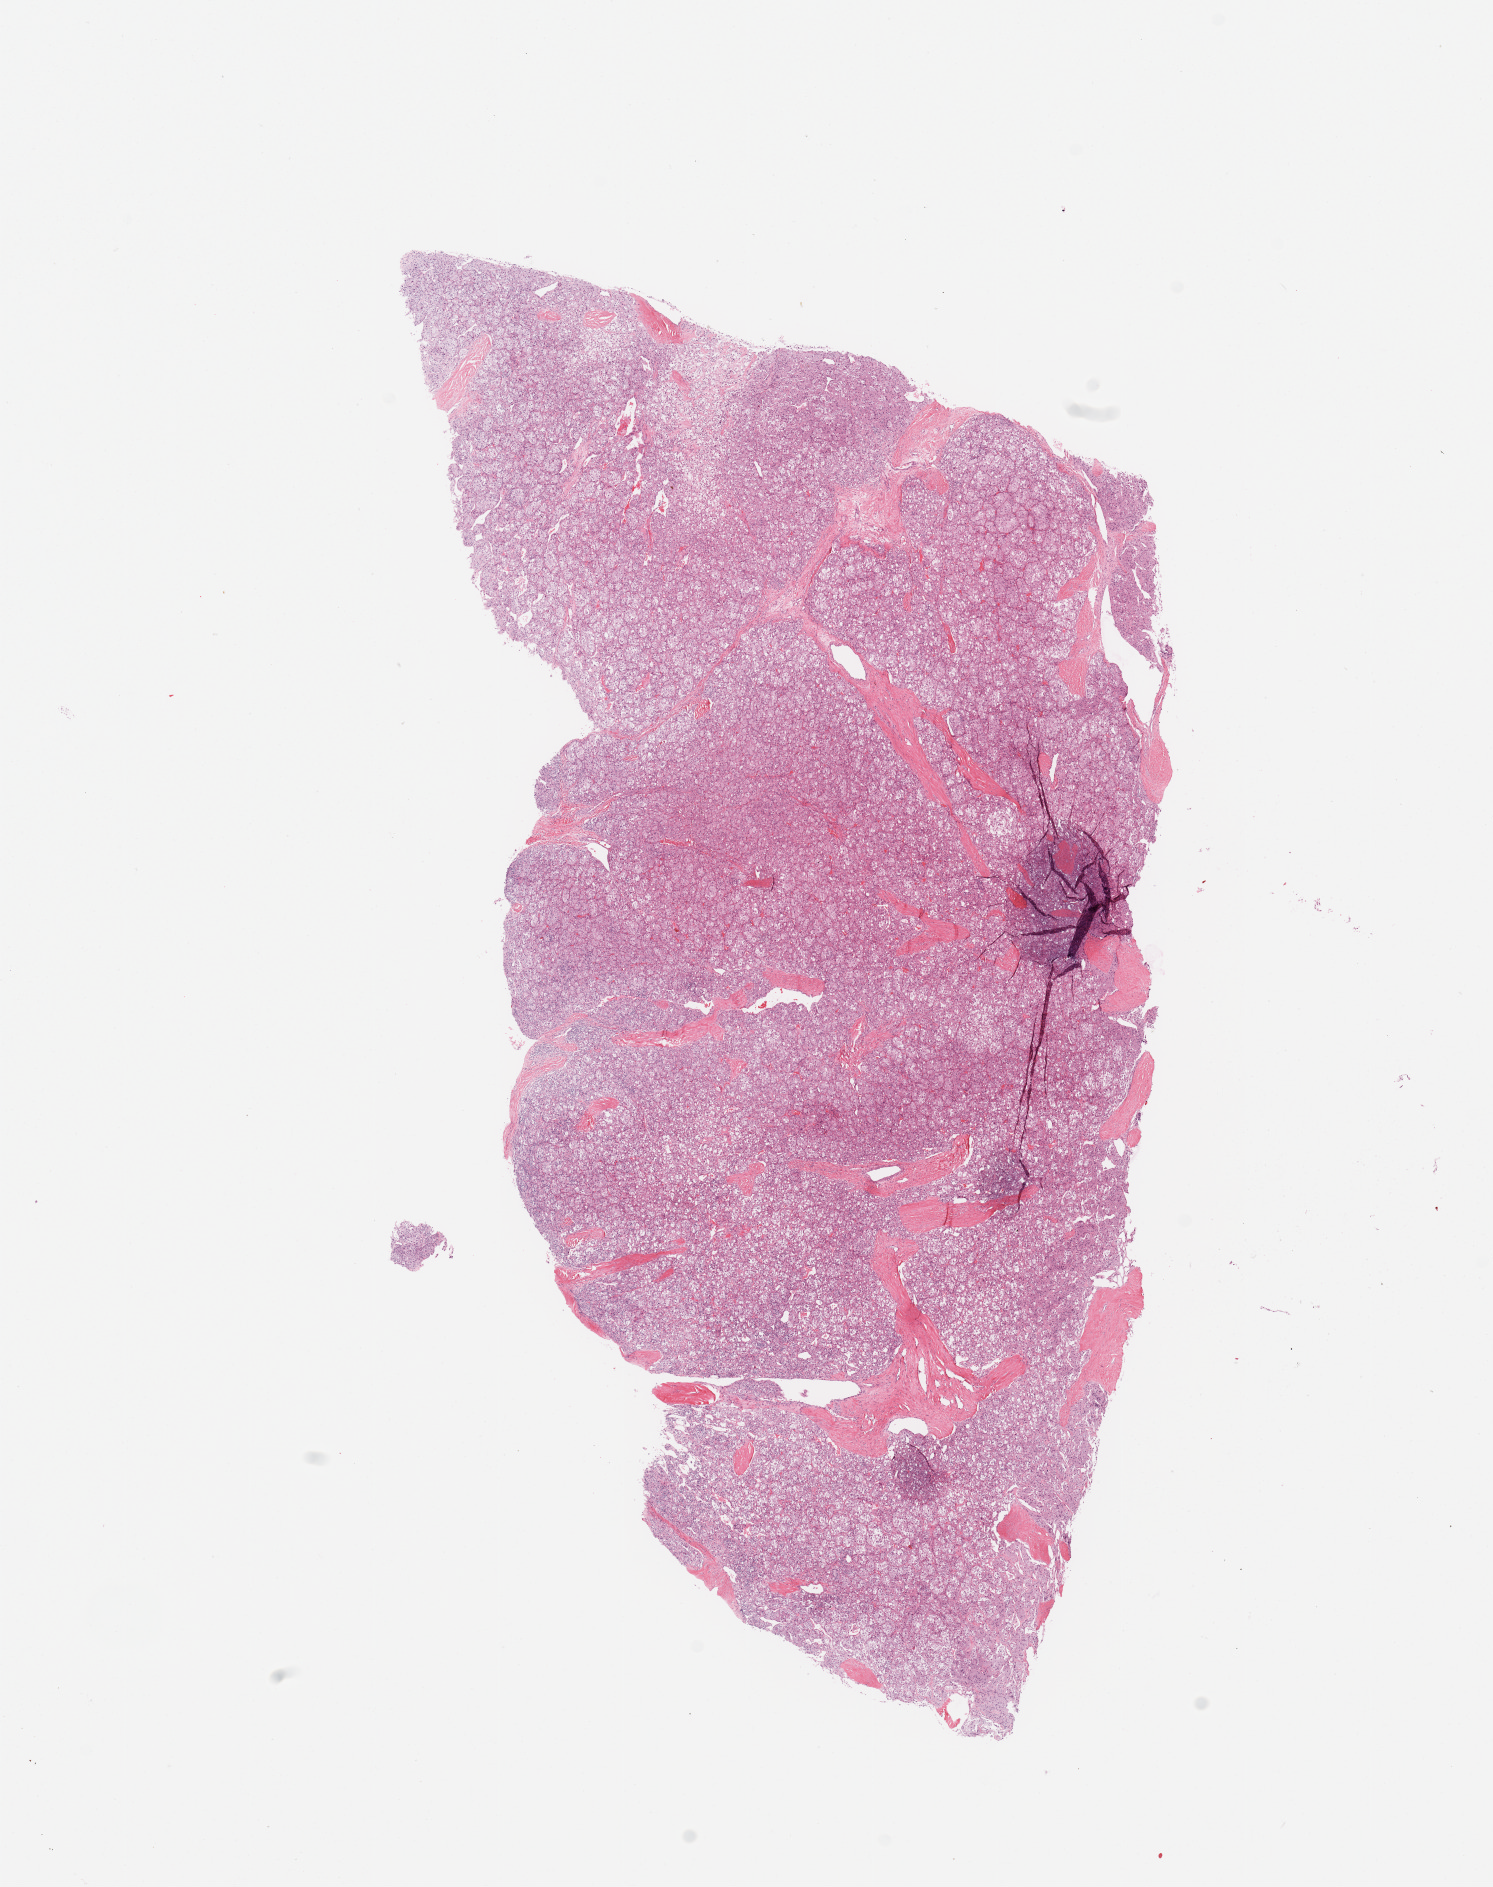
Digitized H&E-stained tissue section (whole slide), whole scanned area (about 11.8 x 14.9 mm, slide scanned at 20x) shown as a low-resolution overview. Patient: male, age 50 years.
Patient diagnosis (cohort enrolment): sarcoma (site not recorded at cohort level). Primary tumour site (as recorded): pelvic.